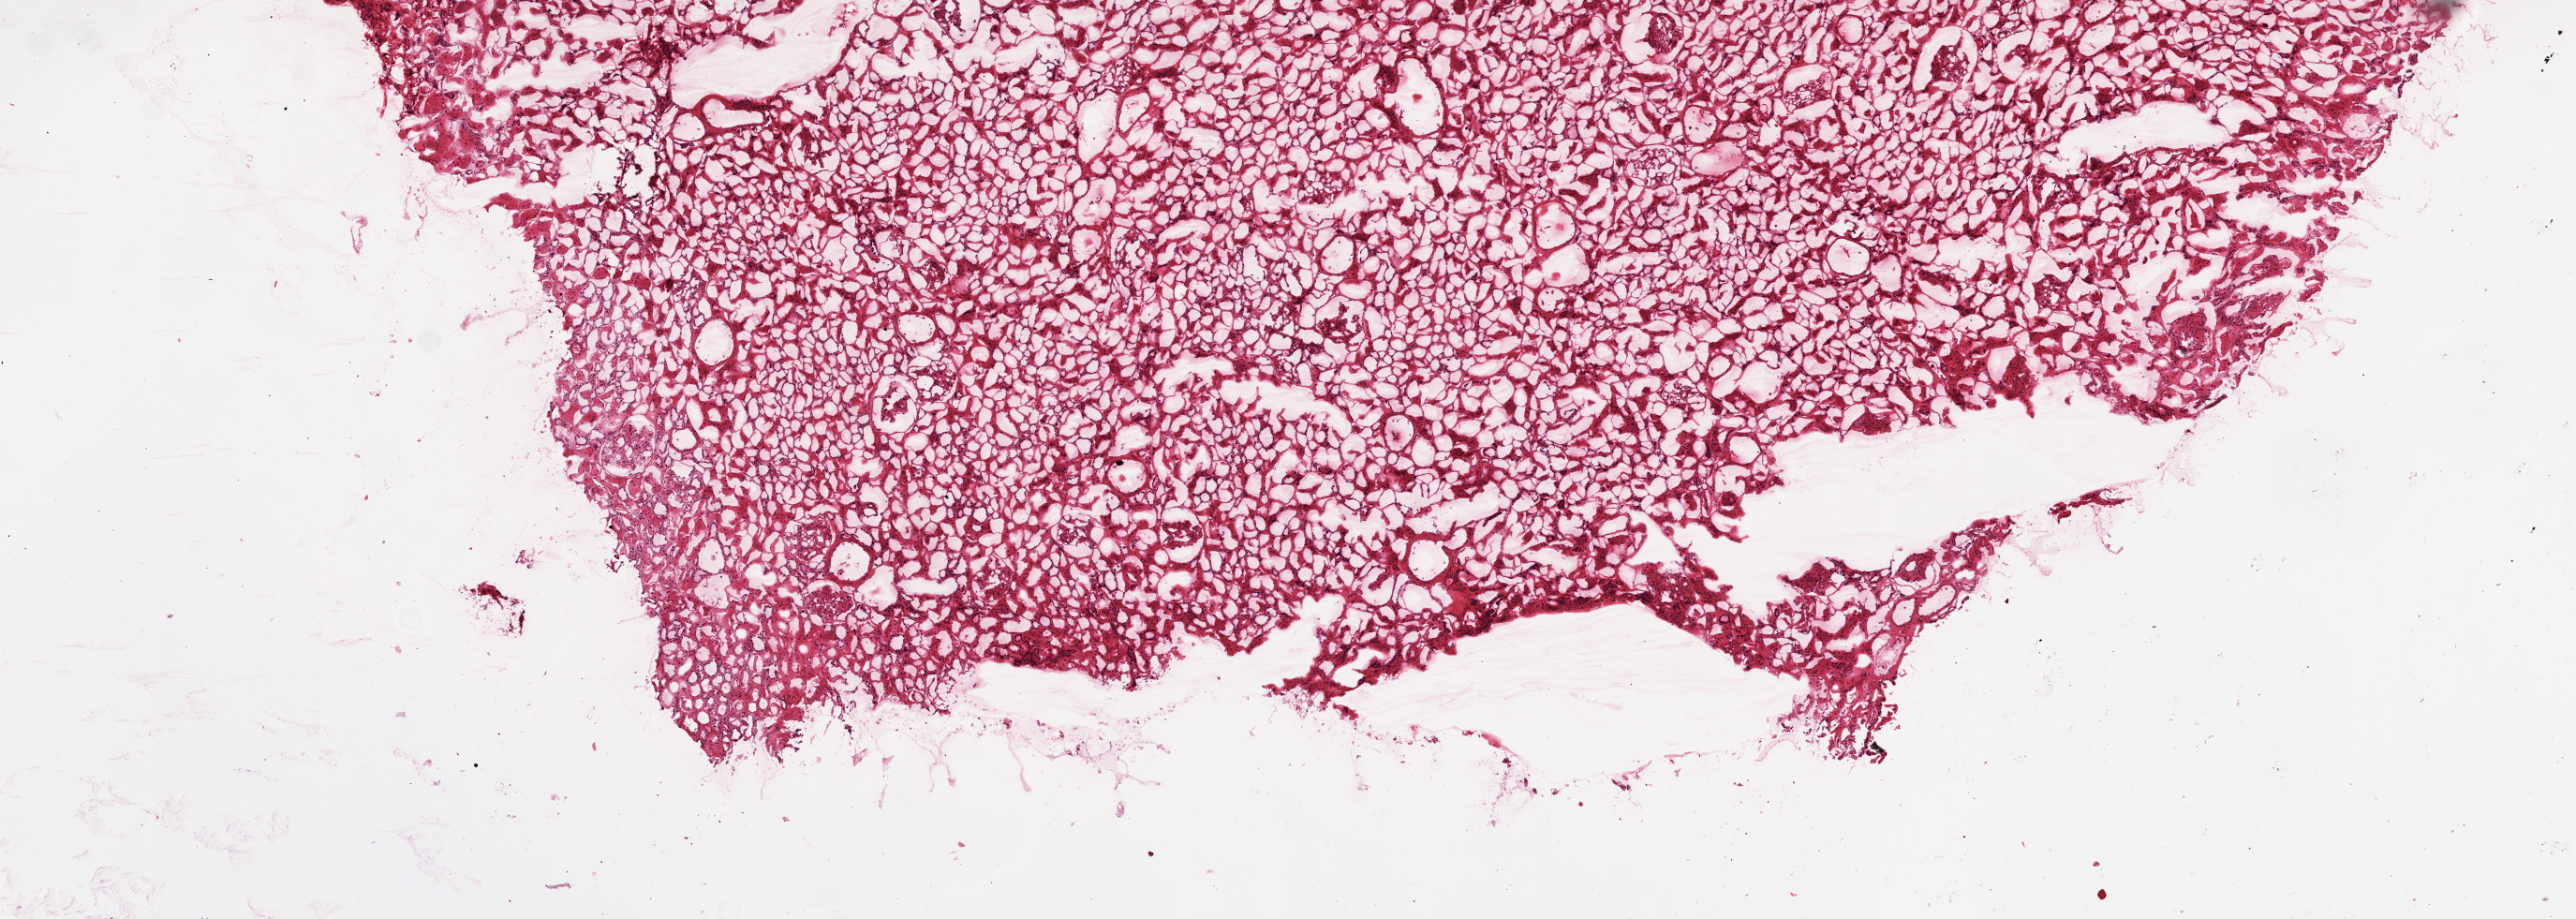
Whole-slide histology image, H&E-stained, whole scanned area (about 11.0 x 3.9 mm) shown as a low-resolution overview. Frozen section from the top of the tissue portion. Solid tissue normal (non-tumour tissue) sample from the kidney. Female, age 74 years at initial diagnosis.
This section: solid tissue normal sample (biorepository sample class). Patient diagnosis: Clear cell adenocarcinoma, NOS.